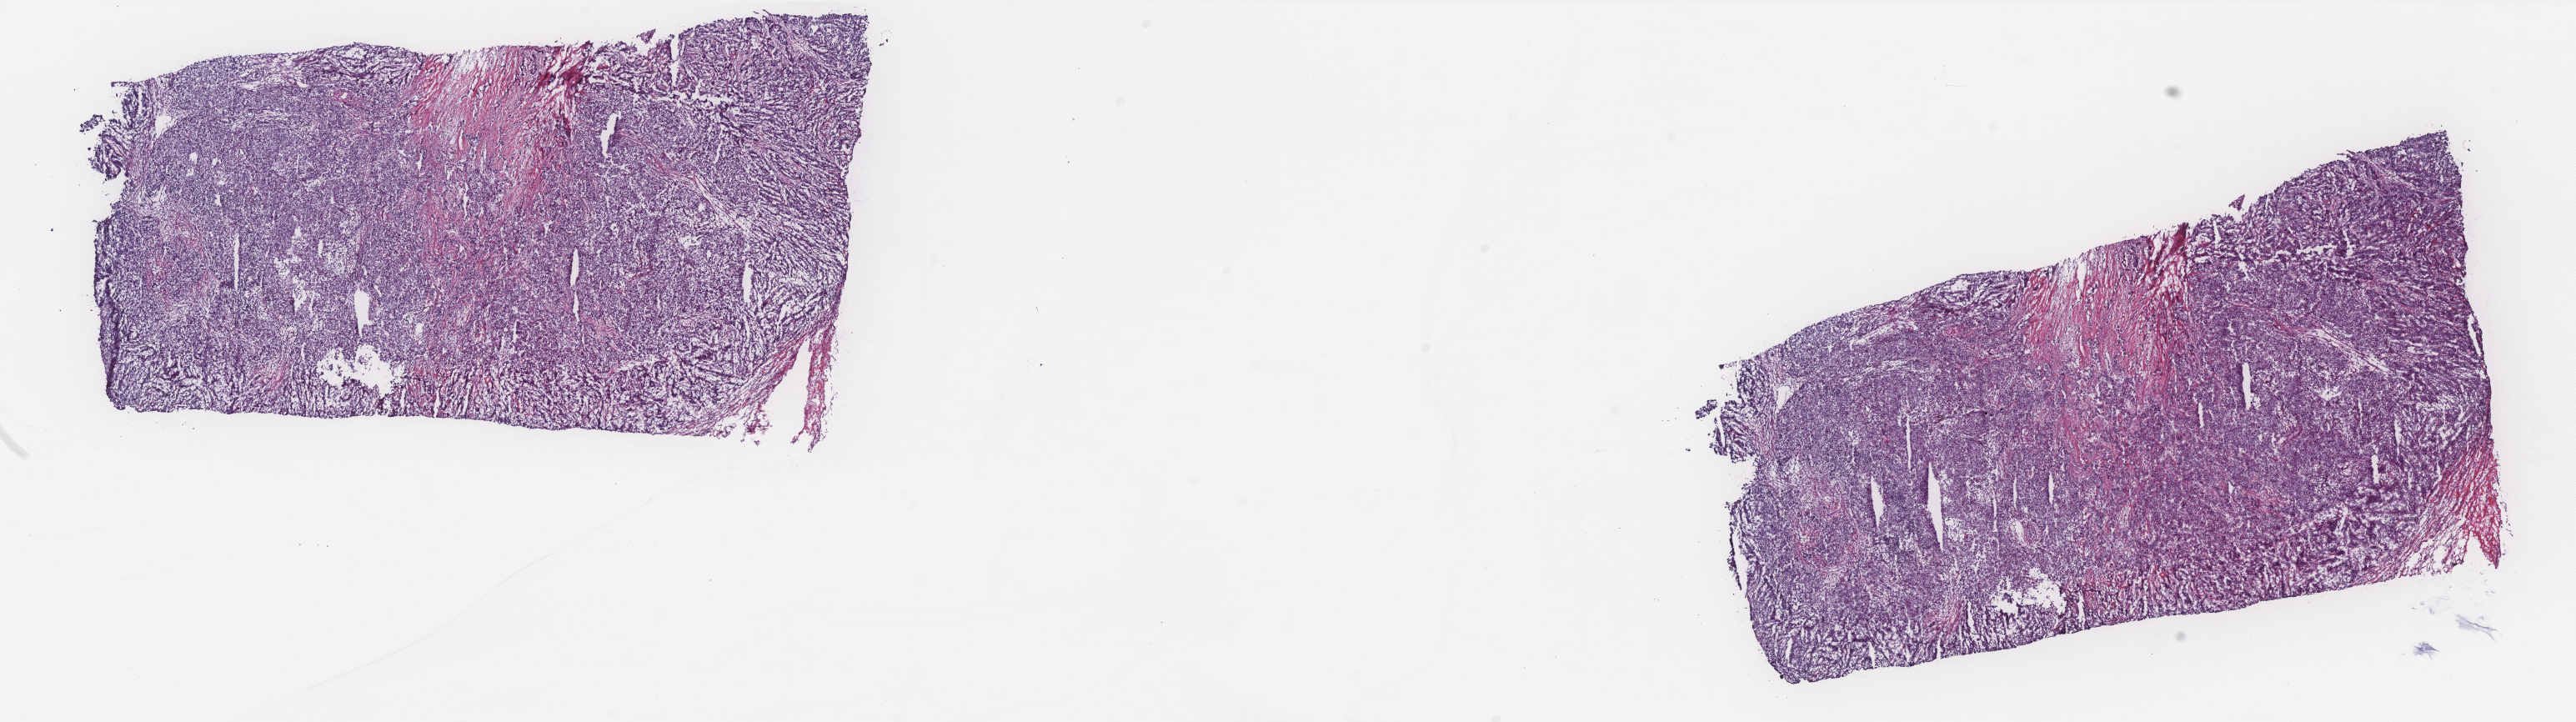
Digitized H&E-stained tissue section (whole slide), a low-resolution overview of the entire scanned area, about 24.8 x 6.9 mm (acquisition: 40x scan). Frozen section from the top of the tissue portion. Sample: primary tumour, breast. Female, age 72 years at initial diagnosis. Slide review estimates, as recorded: tumour cells 85%, tumour nuclei 85%, normal cells 0%, stromal cells 13%, necrosis 2%. Inflammatory infiltration, as recorded: lymphocyte infiltration 2%, monocyte infiltration 1%, neutrophil infiltration 1%.
- lymph nodes positive (case pathology): 0 of 11 examined
- histologic diagnosis: Infiltrating duct carcinoma, NOS
- AJCC pathologic stage: IIA